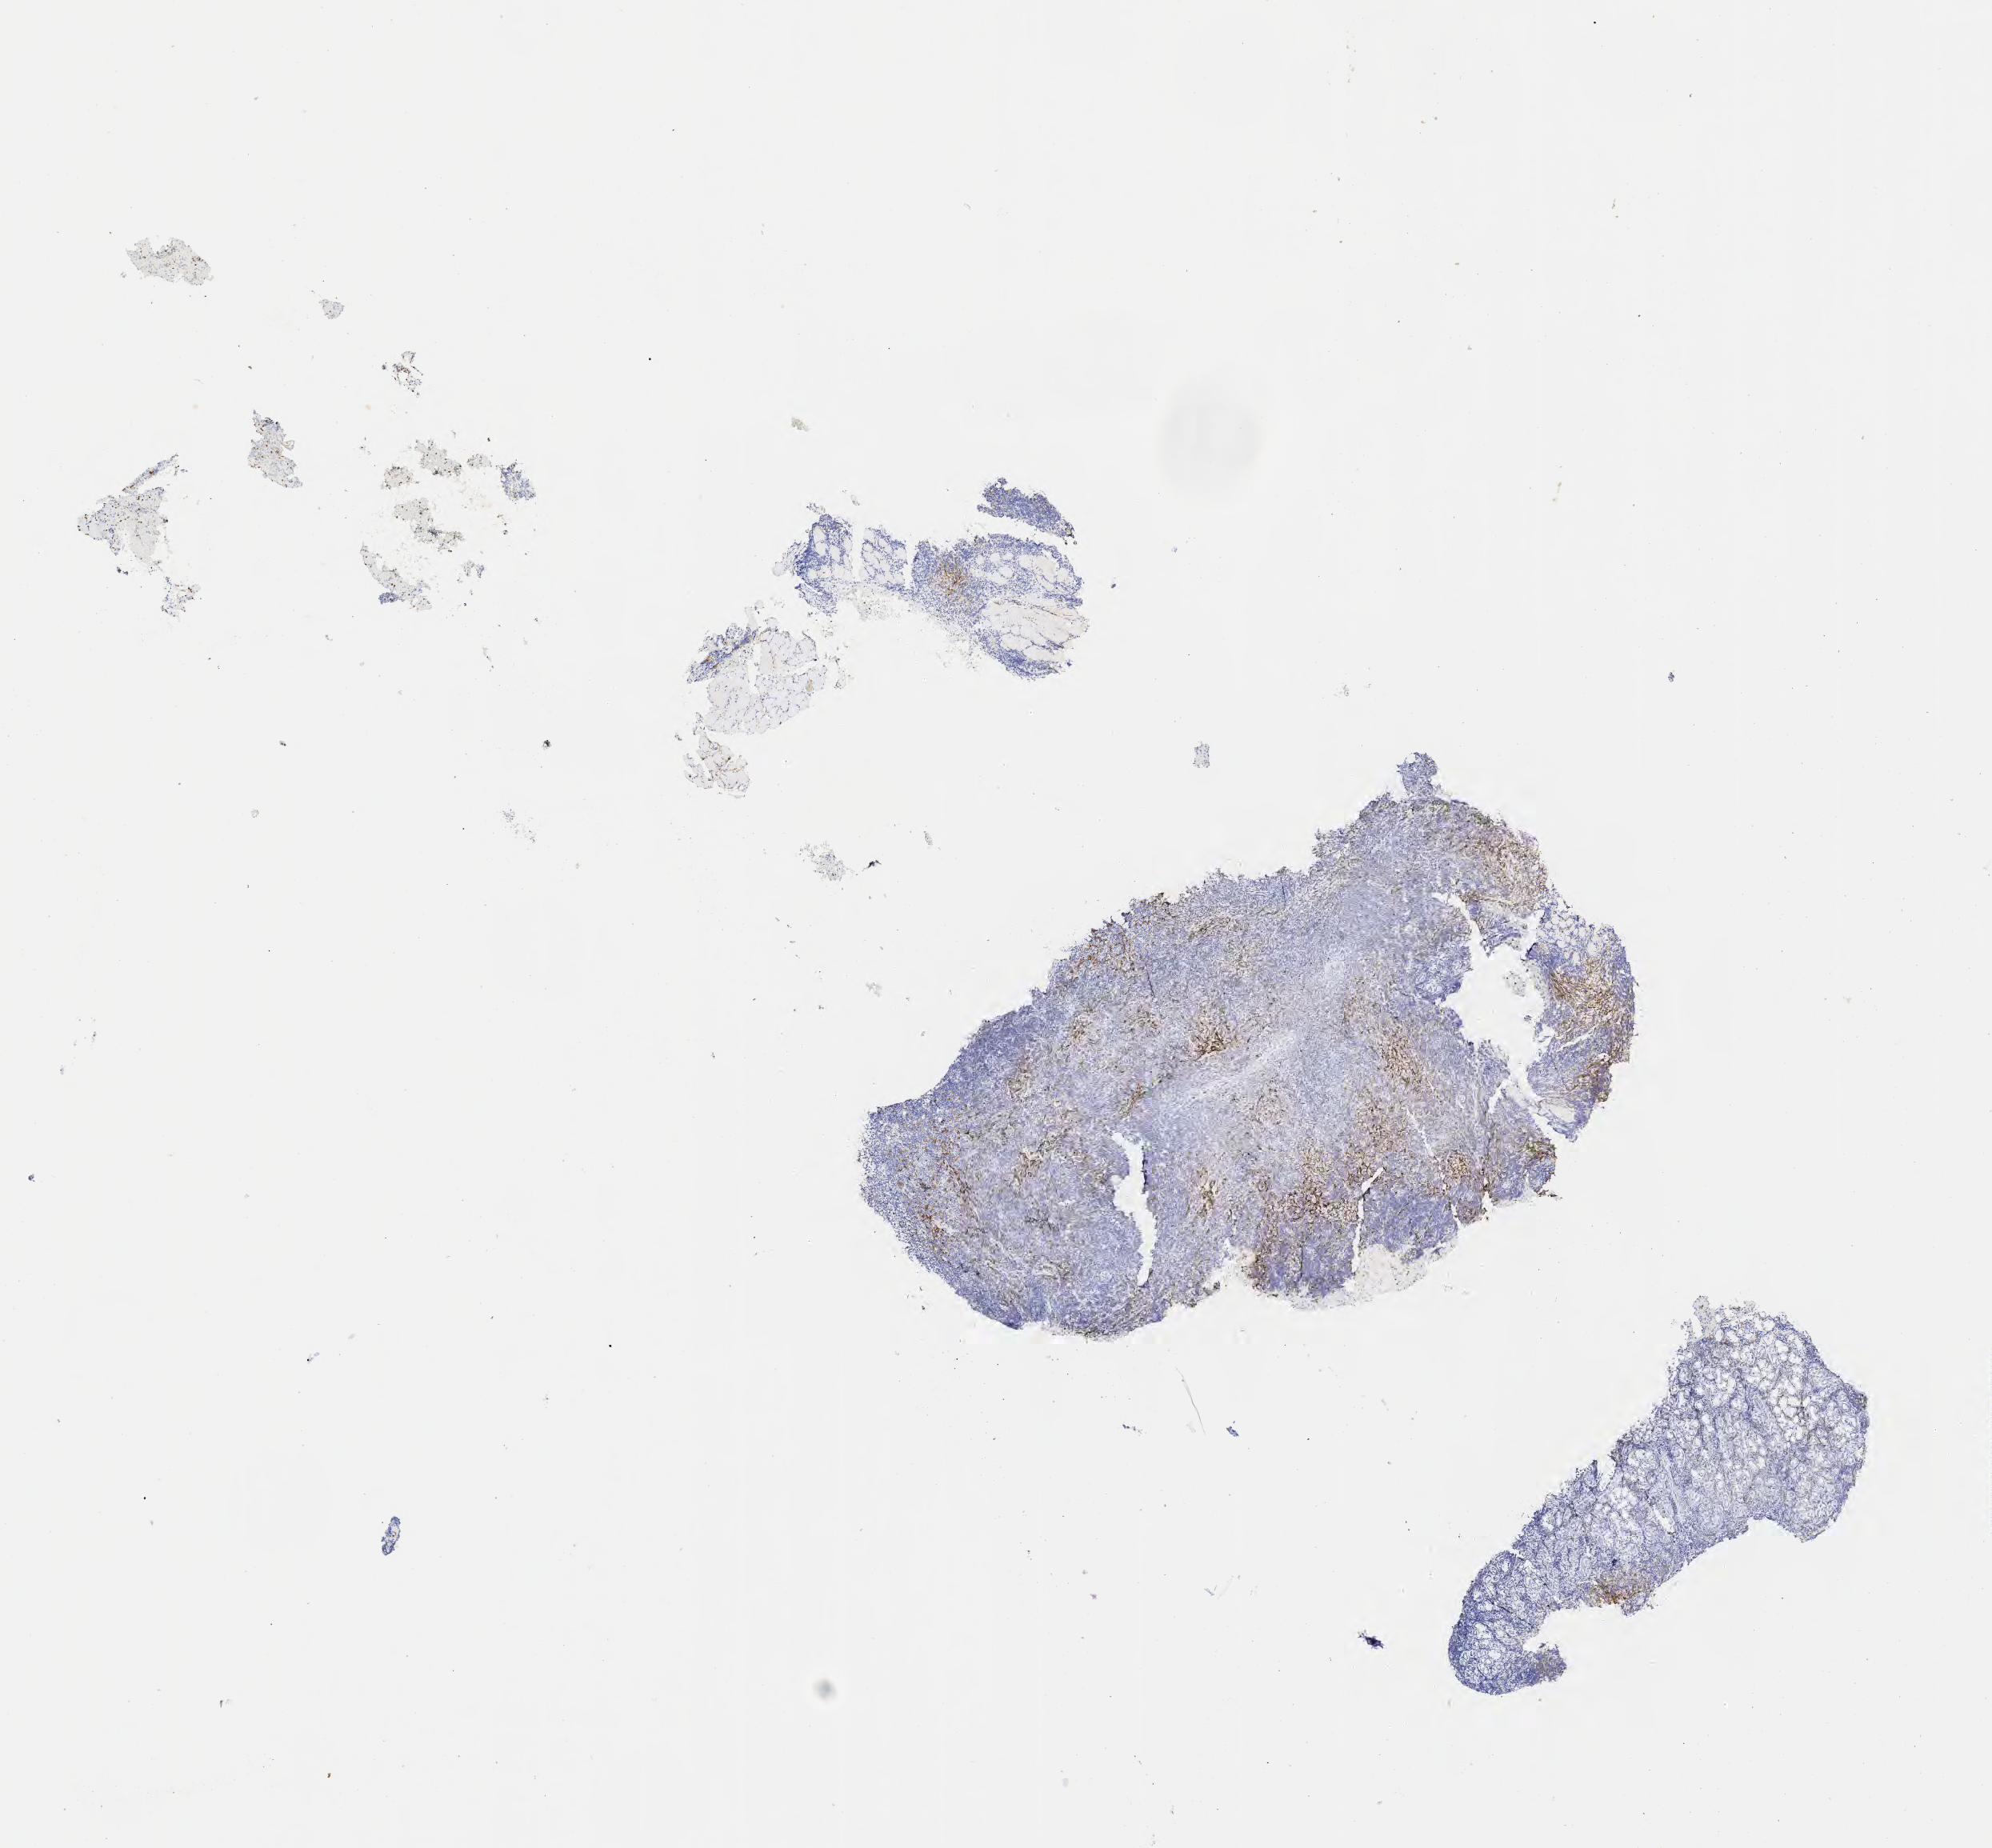
IHC for CD10, whole-slide image, shown as a low-resolution overview of the whole scanned area (about 10.1 x 9.3 mm), tumor tissue. Male patient, 53 years old.
Diagnosis: Diffuse large B-cell lymphoma, NOS.